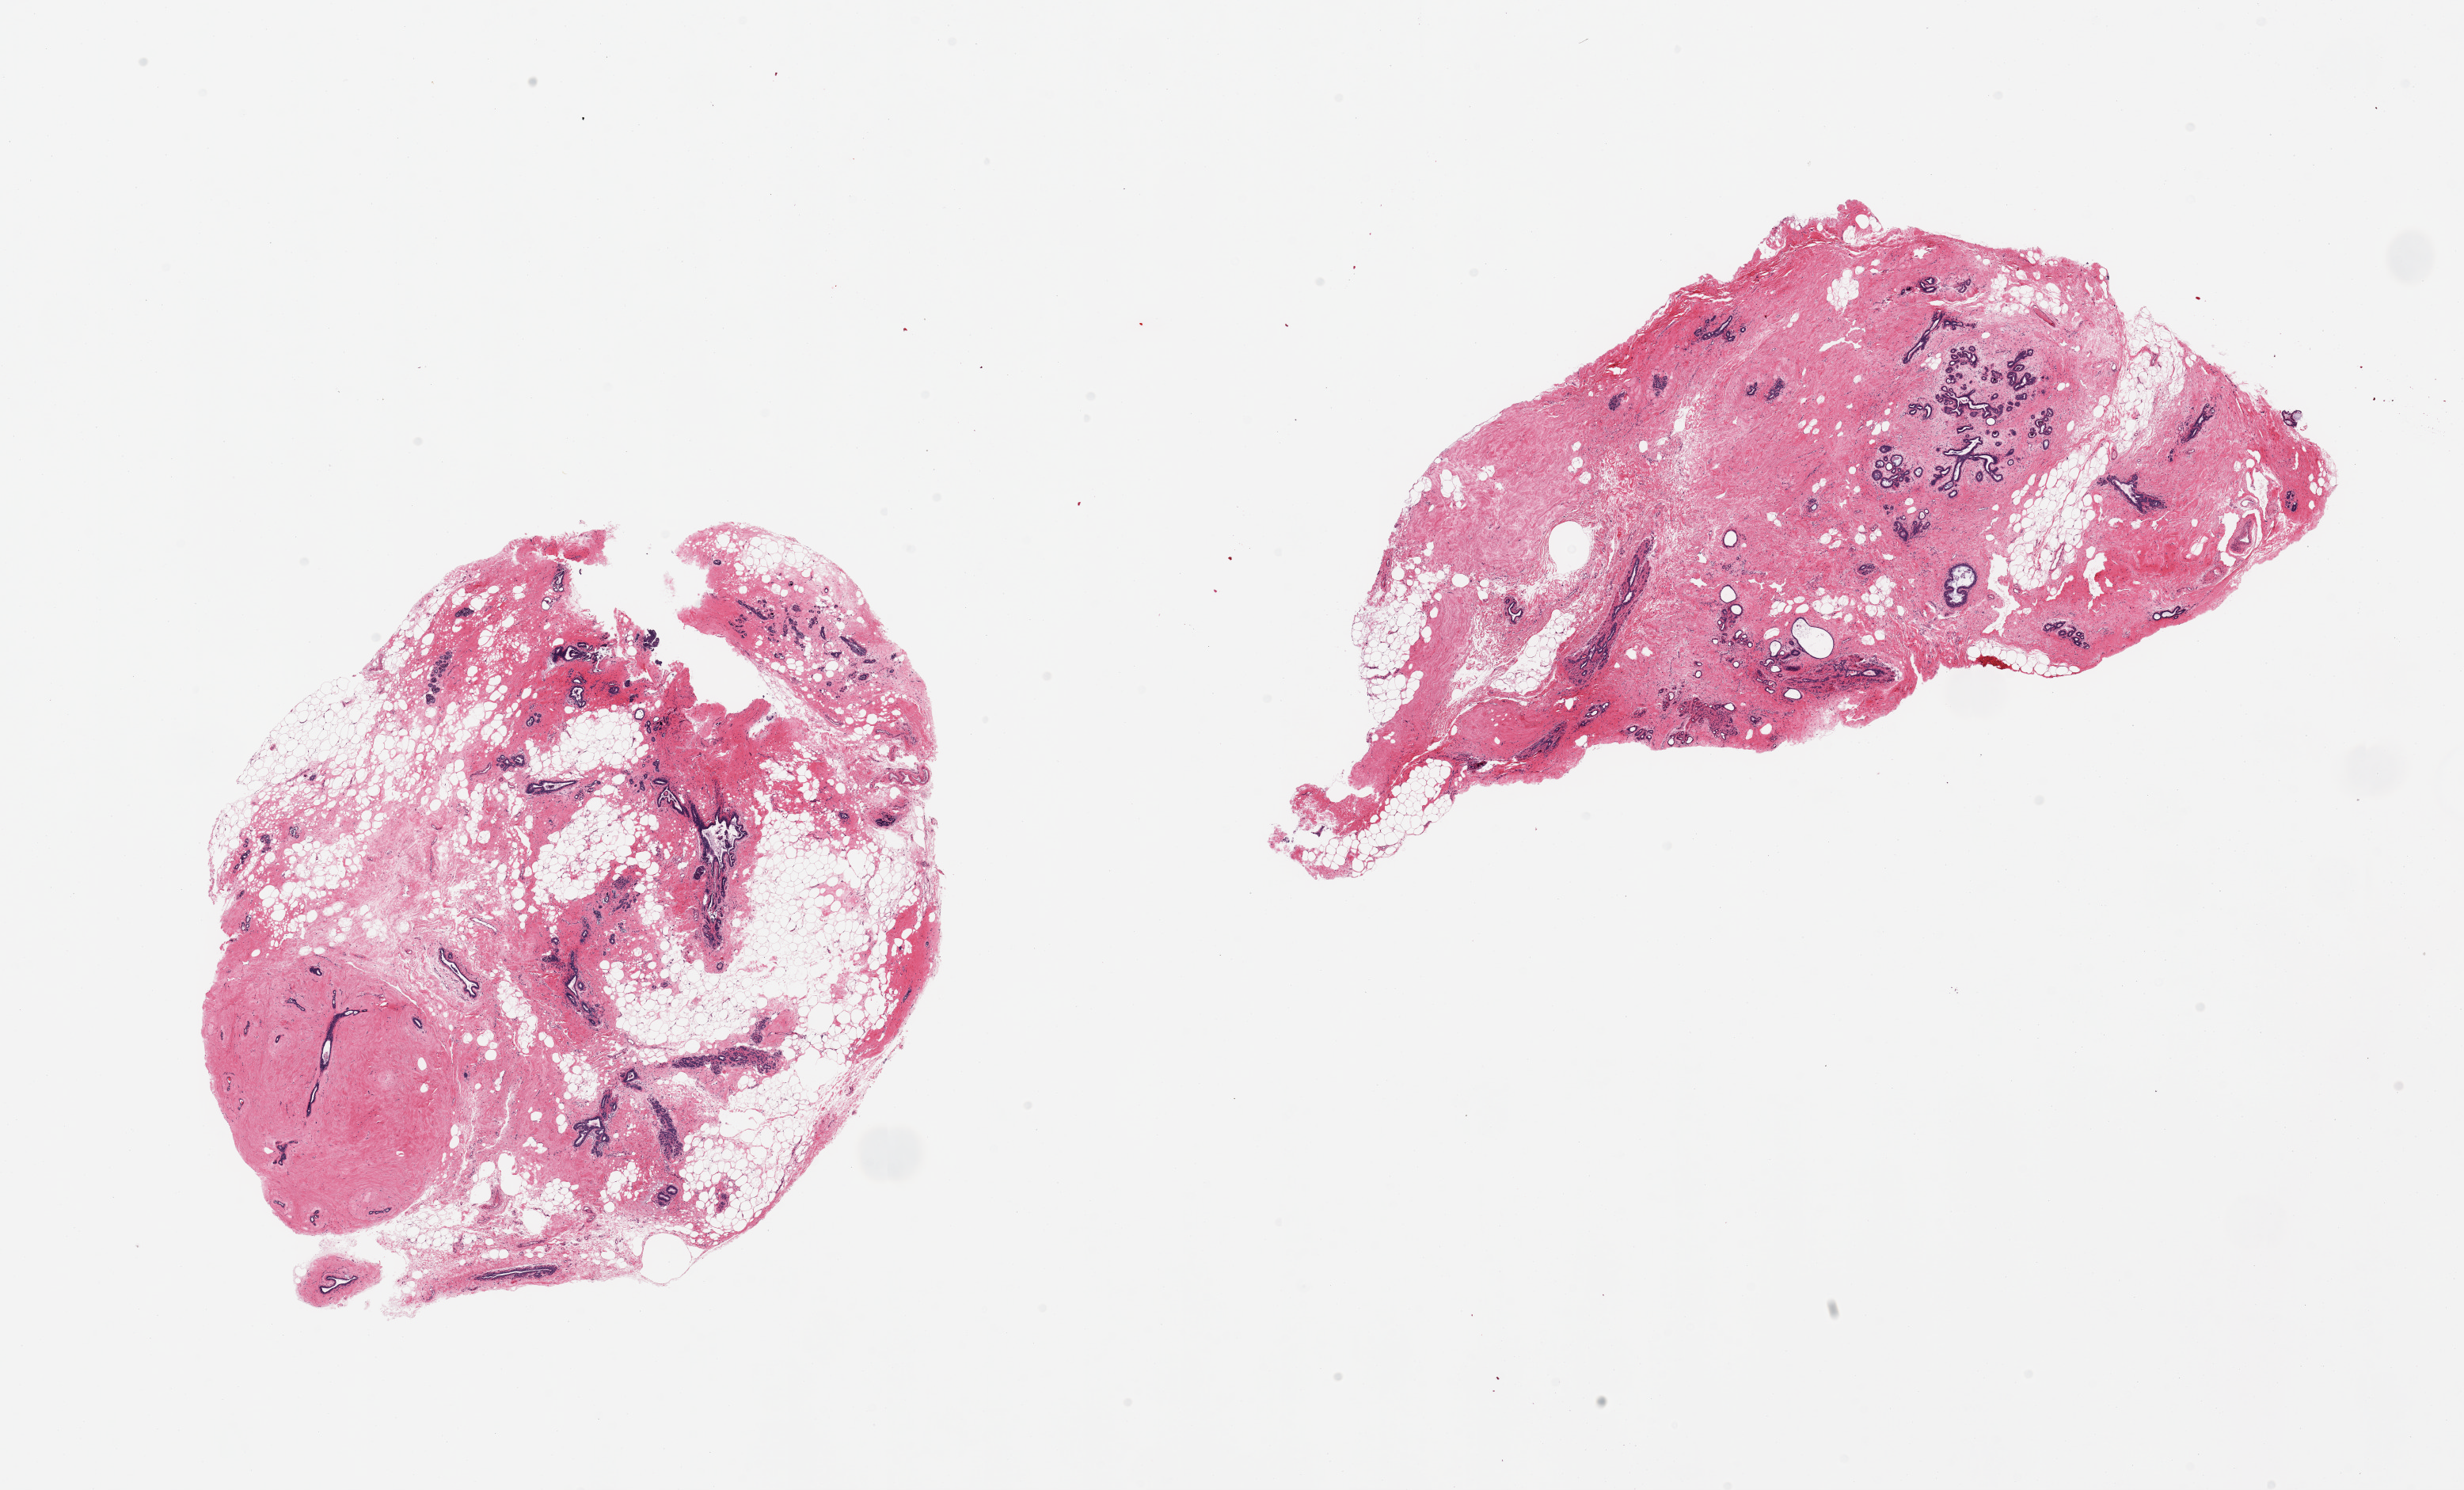
Whole-slide image, haematoxylin and eosin stain, brightfield — low-resolution overview of the scanned area, about 24.6 x 14.9 mm. PAXgene-fixed, paraffin-embedded tissue. Sampled site (target tissue): breast. Donor tissue sample. Donor: female.
• reviewer comment on this tissue sample: 2 pieces, post menopausal duct-lobular units well sampled